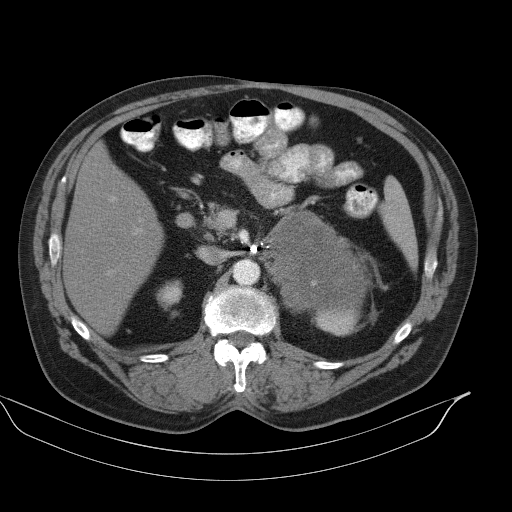
Contrast-enhanced abdominal CT, one axial slice. Position 62 of 92 along the scan axis. 130 kVp. Intravenous contrast given. Soft-tissue window (W 400 / L 40 HU). 512 × 512 image matrix, field of view 449 × 449 mm. Patient: male, 56 years. Case-level facts recorded for this patient, not image findings: diagnosis: adrenocortical carcinoma; tumour side: left adrenal; tumour size at pathology: 15 cm; Ki-67 index: 35 %; stage (as recorded): 4.
Outlined on this slice (semi-automatic segmentation, software-assisted and operator-edited):
- mass: bounding box [x1, y1, x2, y2] px = [269, 213, 367, 309]